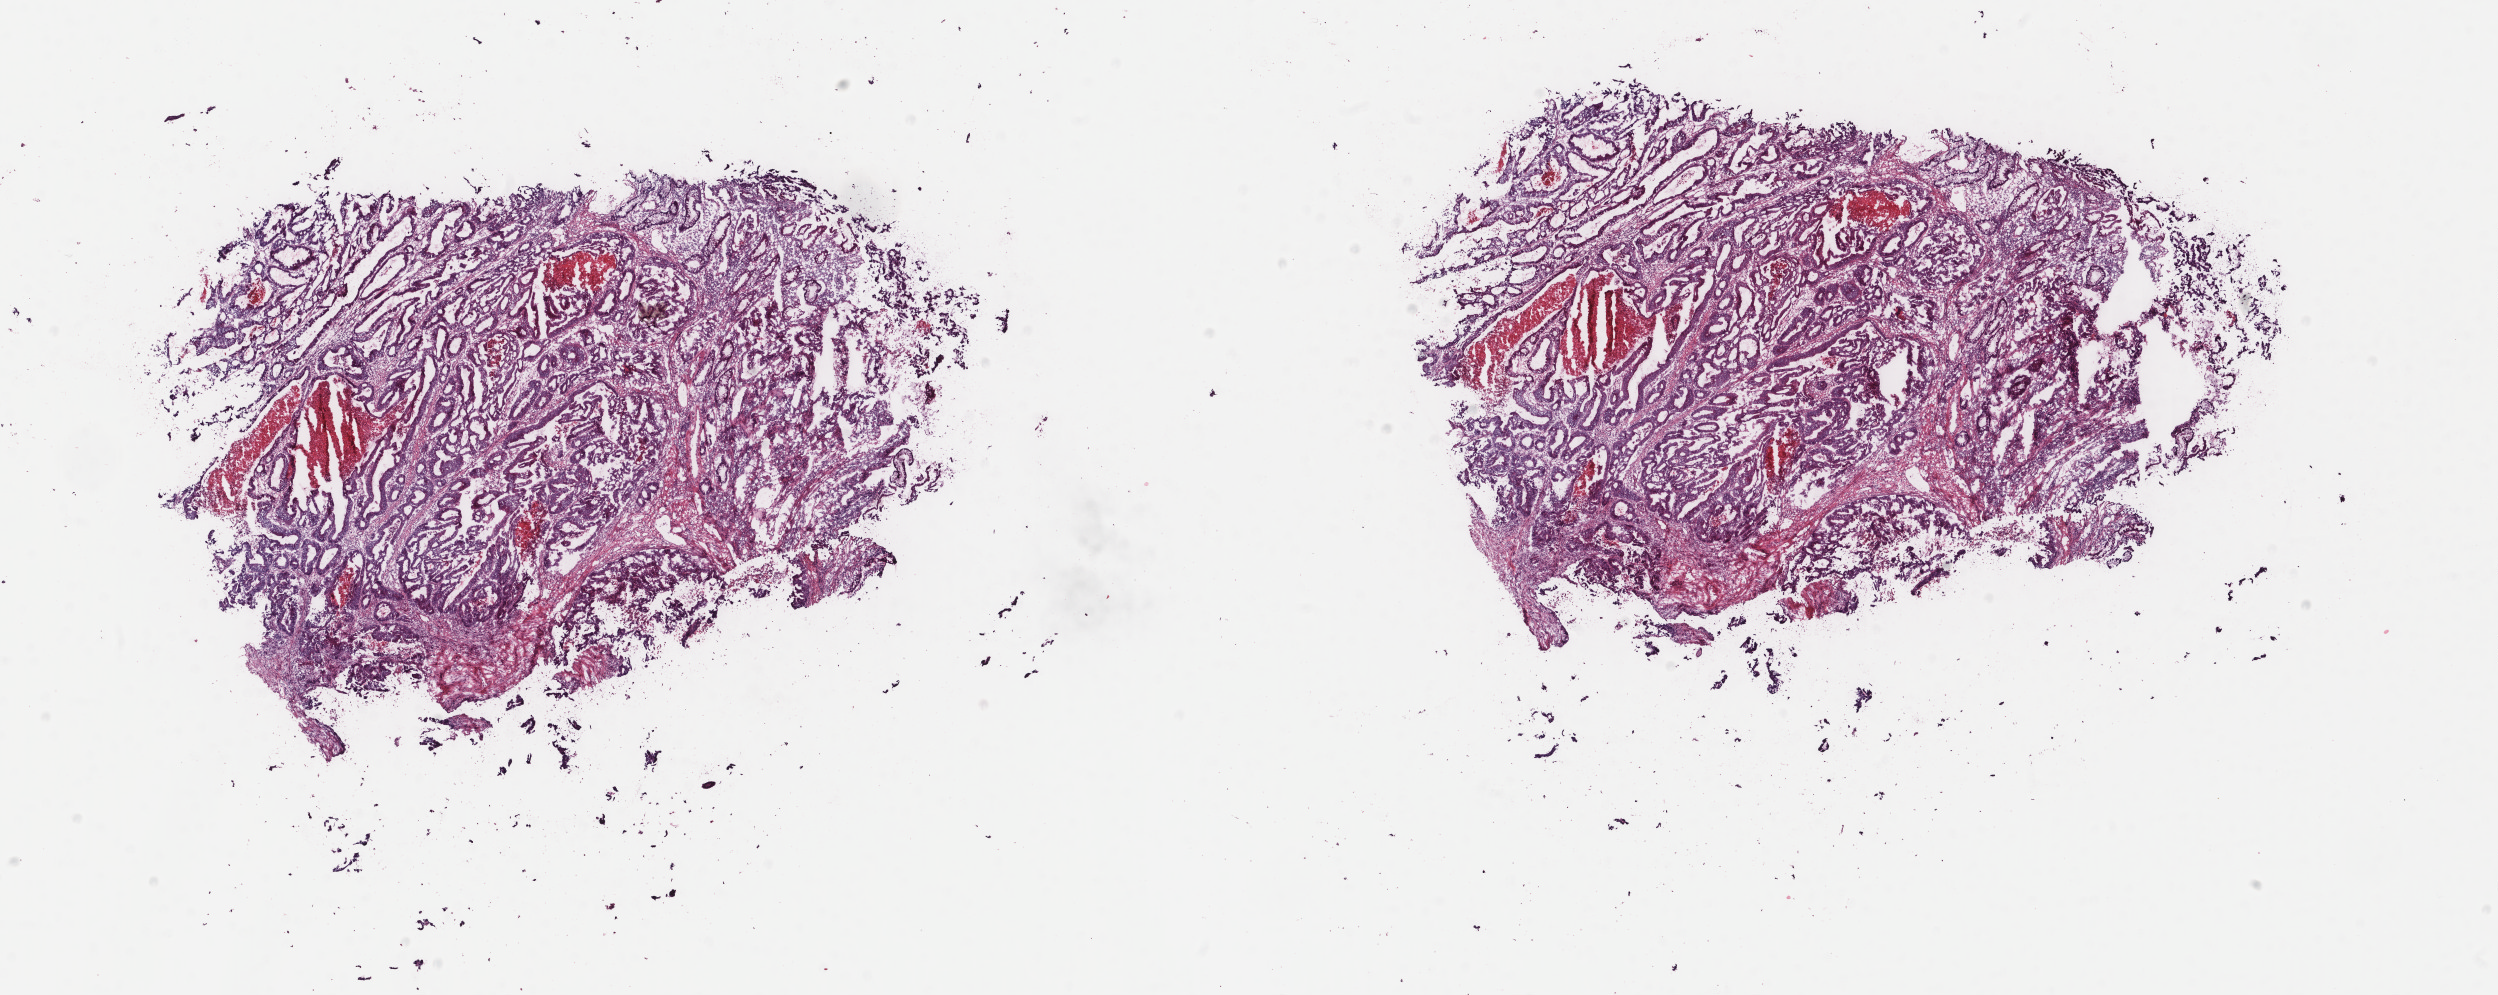
Whole-slide histology image, H&E-stained — shown as a low-resolution overview of the whole scanned area (about 19.8 x 7.9 mm). Frozen section from the bottom of the tissue portion. Sample: primary tumour, colon. Female, age 71 years at initial diagnosis.
Pathologic diagnosis: Adenocarcinoma, NOS (ascending colon).